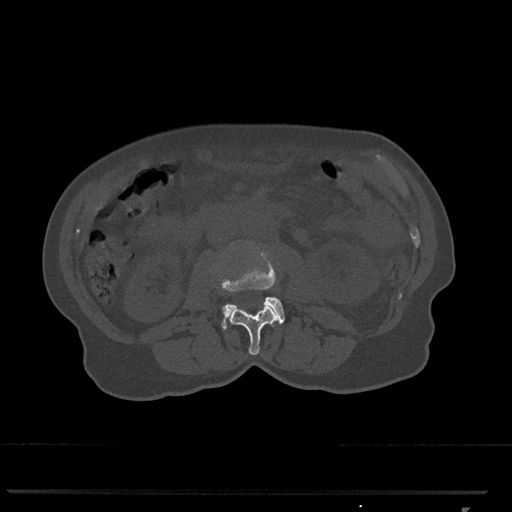
CT including the spine, one axial slice; slice 305 of 793 in the series (ordered by position); reconstruction kernel Br40s/3; bone window (W 1800 / L 400 HU); 0.5 mm slice thickness; 512 × 512 image matrix, field of view 380 × 380 mm. Patient: female, 62 years. Case-level facts recorded for this patient, not image findings: primary cancer: renal.
Structures marked on this image (semi-automatic segmentation, software-assisted and operator-edited):
- L2 vertebra: bounding box [x1, y1, x2, y2] px = [229, 304, 278, 355]
- L3 vertebra: [221, 248, 285, 330]